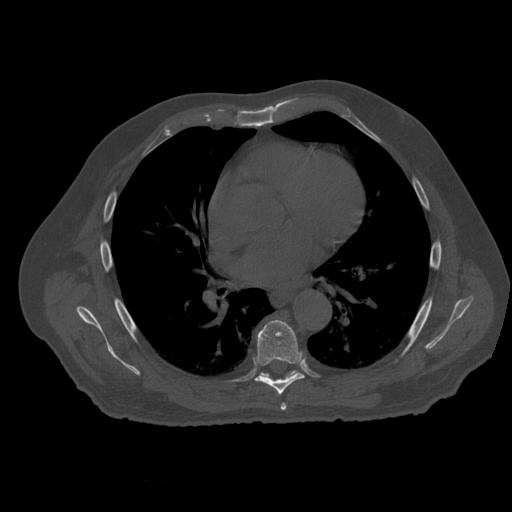
CT including the spine, one axial slice; position 358 of 399 along the scan axis; 120 kVp; bone window (W 1800 / L 400 HU); 1.25 mm slice thickness; 512 × 512 image matrix, field of view 407 × 407 mm. Patient age 73 years. Case-level facts recorded for this patient, not image findings: primary cancer: prostate; vertebrae with lytic lesions (as recorded): L2.
Structures marked on this image (semi-automatically segmented with operator editing):
- T6 vertebra: bounding box <281,404,287,412> (left, top, right, bottom; pixels)
- T7 vertebra: <254,320,305,395>
- T8 vertebra: <261,371,297,377>